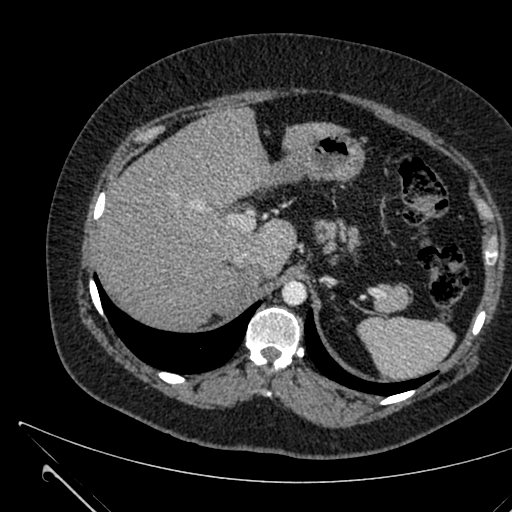
Contrast-enhanced abdominal CT, one axial slice. Position 480 of 731 along the scan axis. 120 kVp. Intravenous contrast given. Soft-tissue window (W 400 / L 40 HU). 512 × 512 image matrix, field of view 376 × 376 mm. Female patient, age 36 years. From the clinical record (not read from this slice): diagnosis: adrenocortical carcinoma; tumour side: right adrenal; tumour size at pathology: 10 cm; Ki-67 index: 20 %; stage (as recorded): 4.
Outlined on this slice (semi-automatically segmented with operator editing):
- mass: box from (x=218, y=267) to (x=259, y=316) px